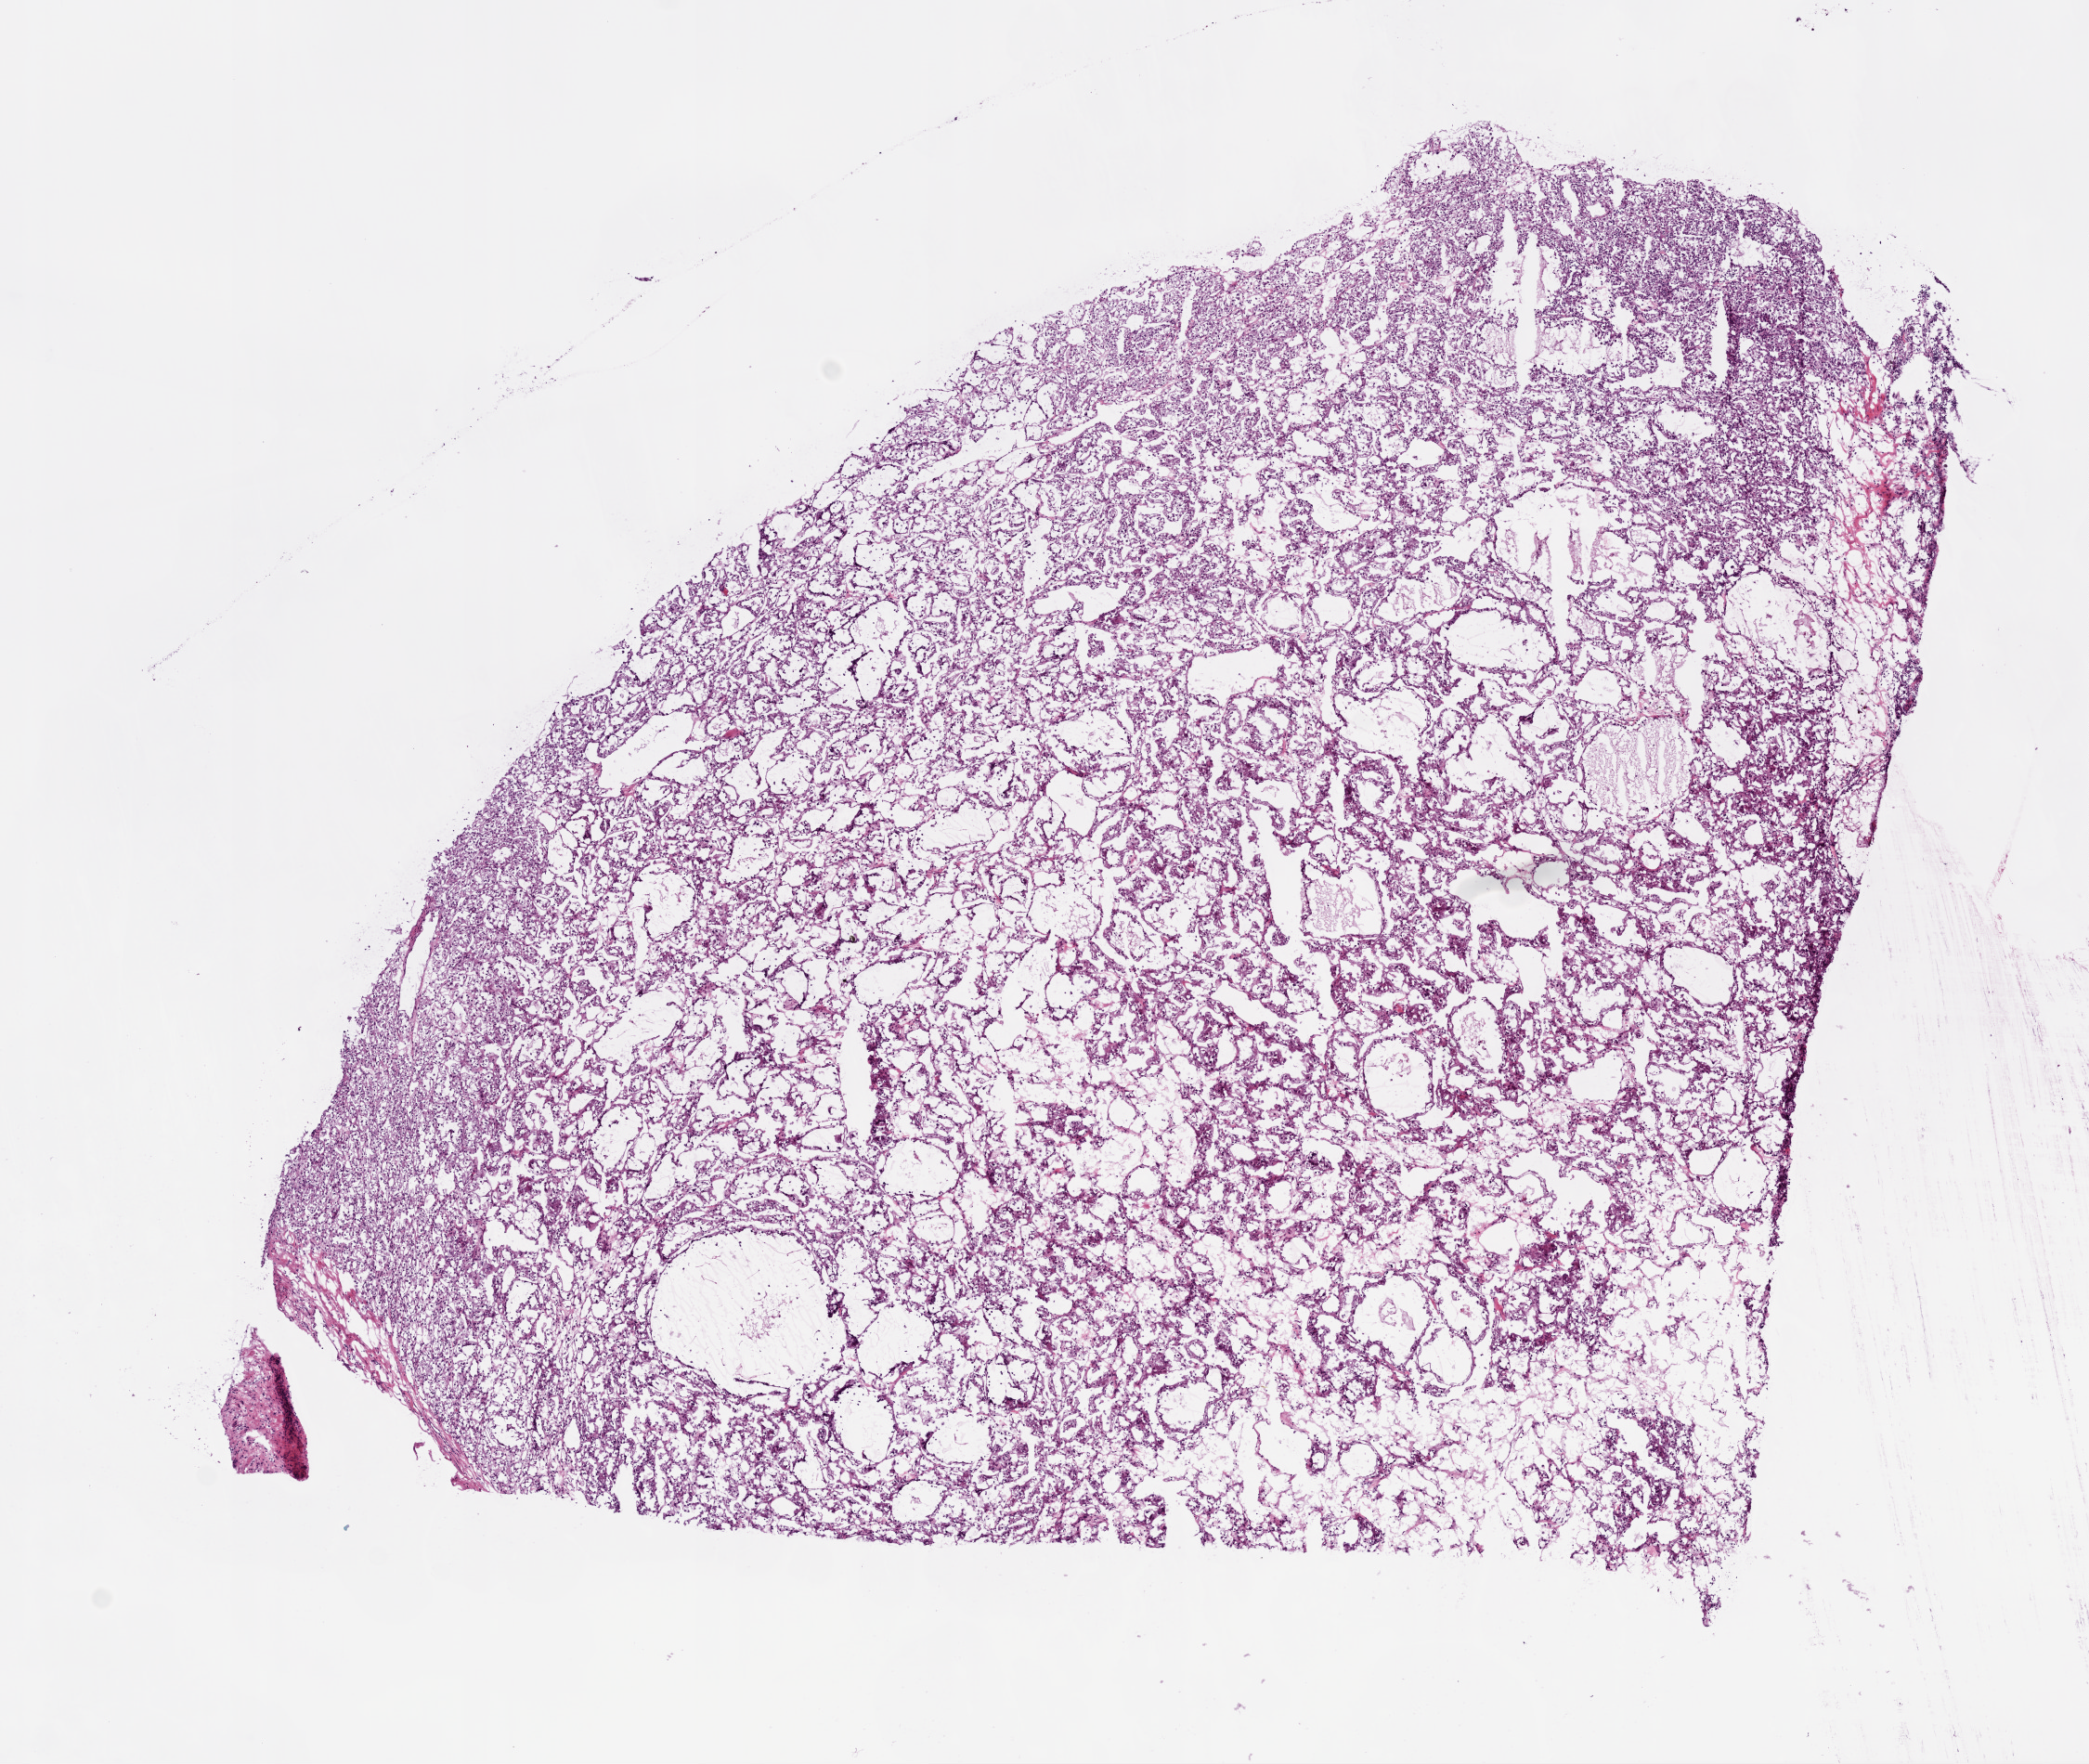
Digitized Hematoxylin and eosin (H&E) stained tissue section (whole slide) — a low-resolution overview of the entire scanned area, about 9.0 x 7.6 mm (acquisition: 20x scan). Frozen section from the bottom of the tissue portion. Sample: primary tumour, kidney. Patient: male, age at initial diagnosis 71 years. Histologic grade: G2 (moderately differentiated). Pathologist review of this section (percent, as recorded): tumour cells 90%, tumour nuclei 80%, normal cells 0%, stromal cells 10%, necrosis 0%.
• diagnosis: Clear cell adenocarcinoma, NOS
• AJCC pathologic stage: I